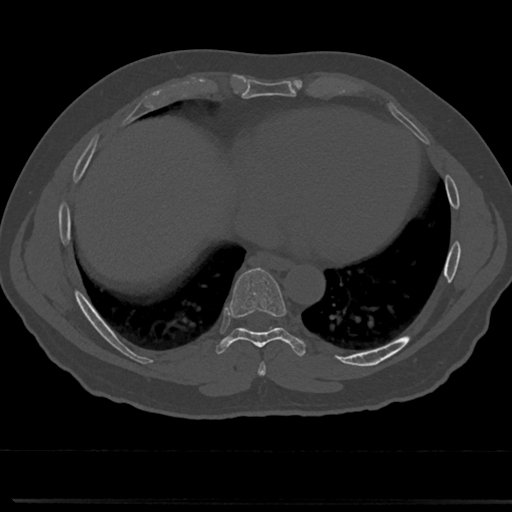
CT including the spine, one axial slice; slice 352 of 817 in the series (ordered by position); 120 kVp; bone window (W 1800 / L 400 HU); 0.5 mm slice thickness; 512 × 512 image matrix, field of view 355 × 355 mm. Patient: male, 61 years. From the clinical record (not read from this slice): primary cancer: prostate.
Structures marked on this image (semi-automatically segmented with operator editing):
- T7 vertebra: box from (x=253, y=336) to (x=275, y=375) px
- T8 vertebra: (x=221, y=271)–(x=297, y=346)